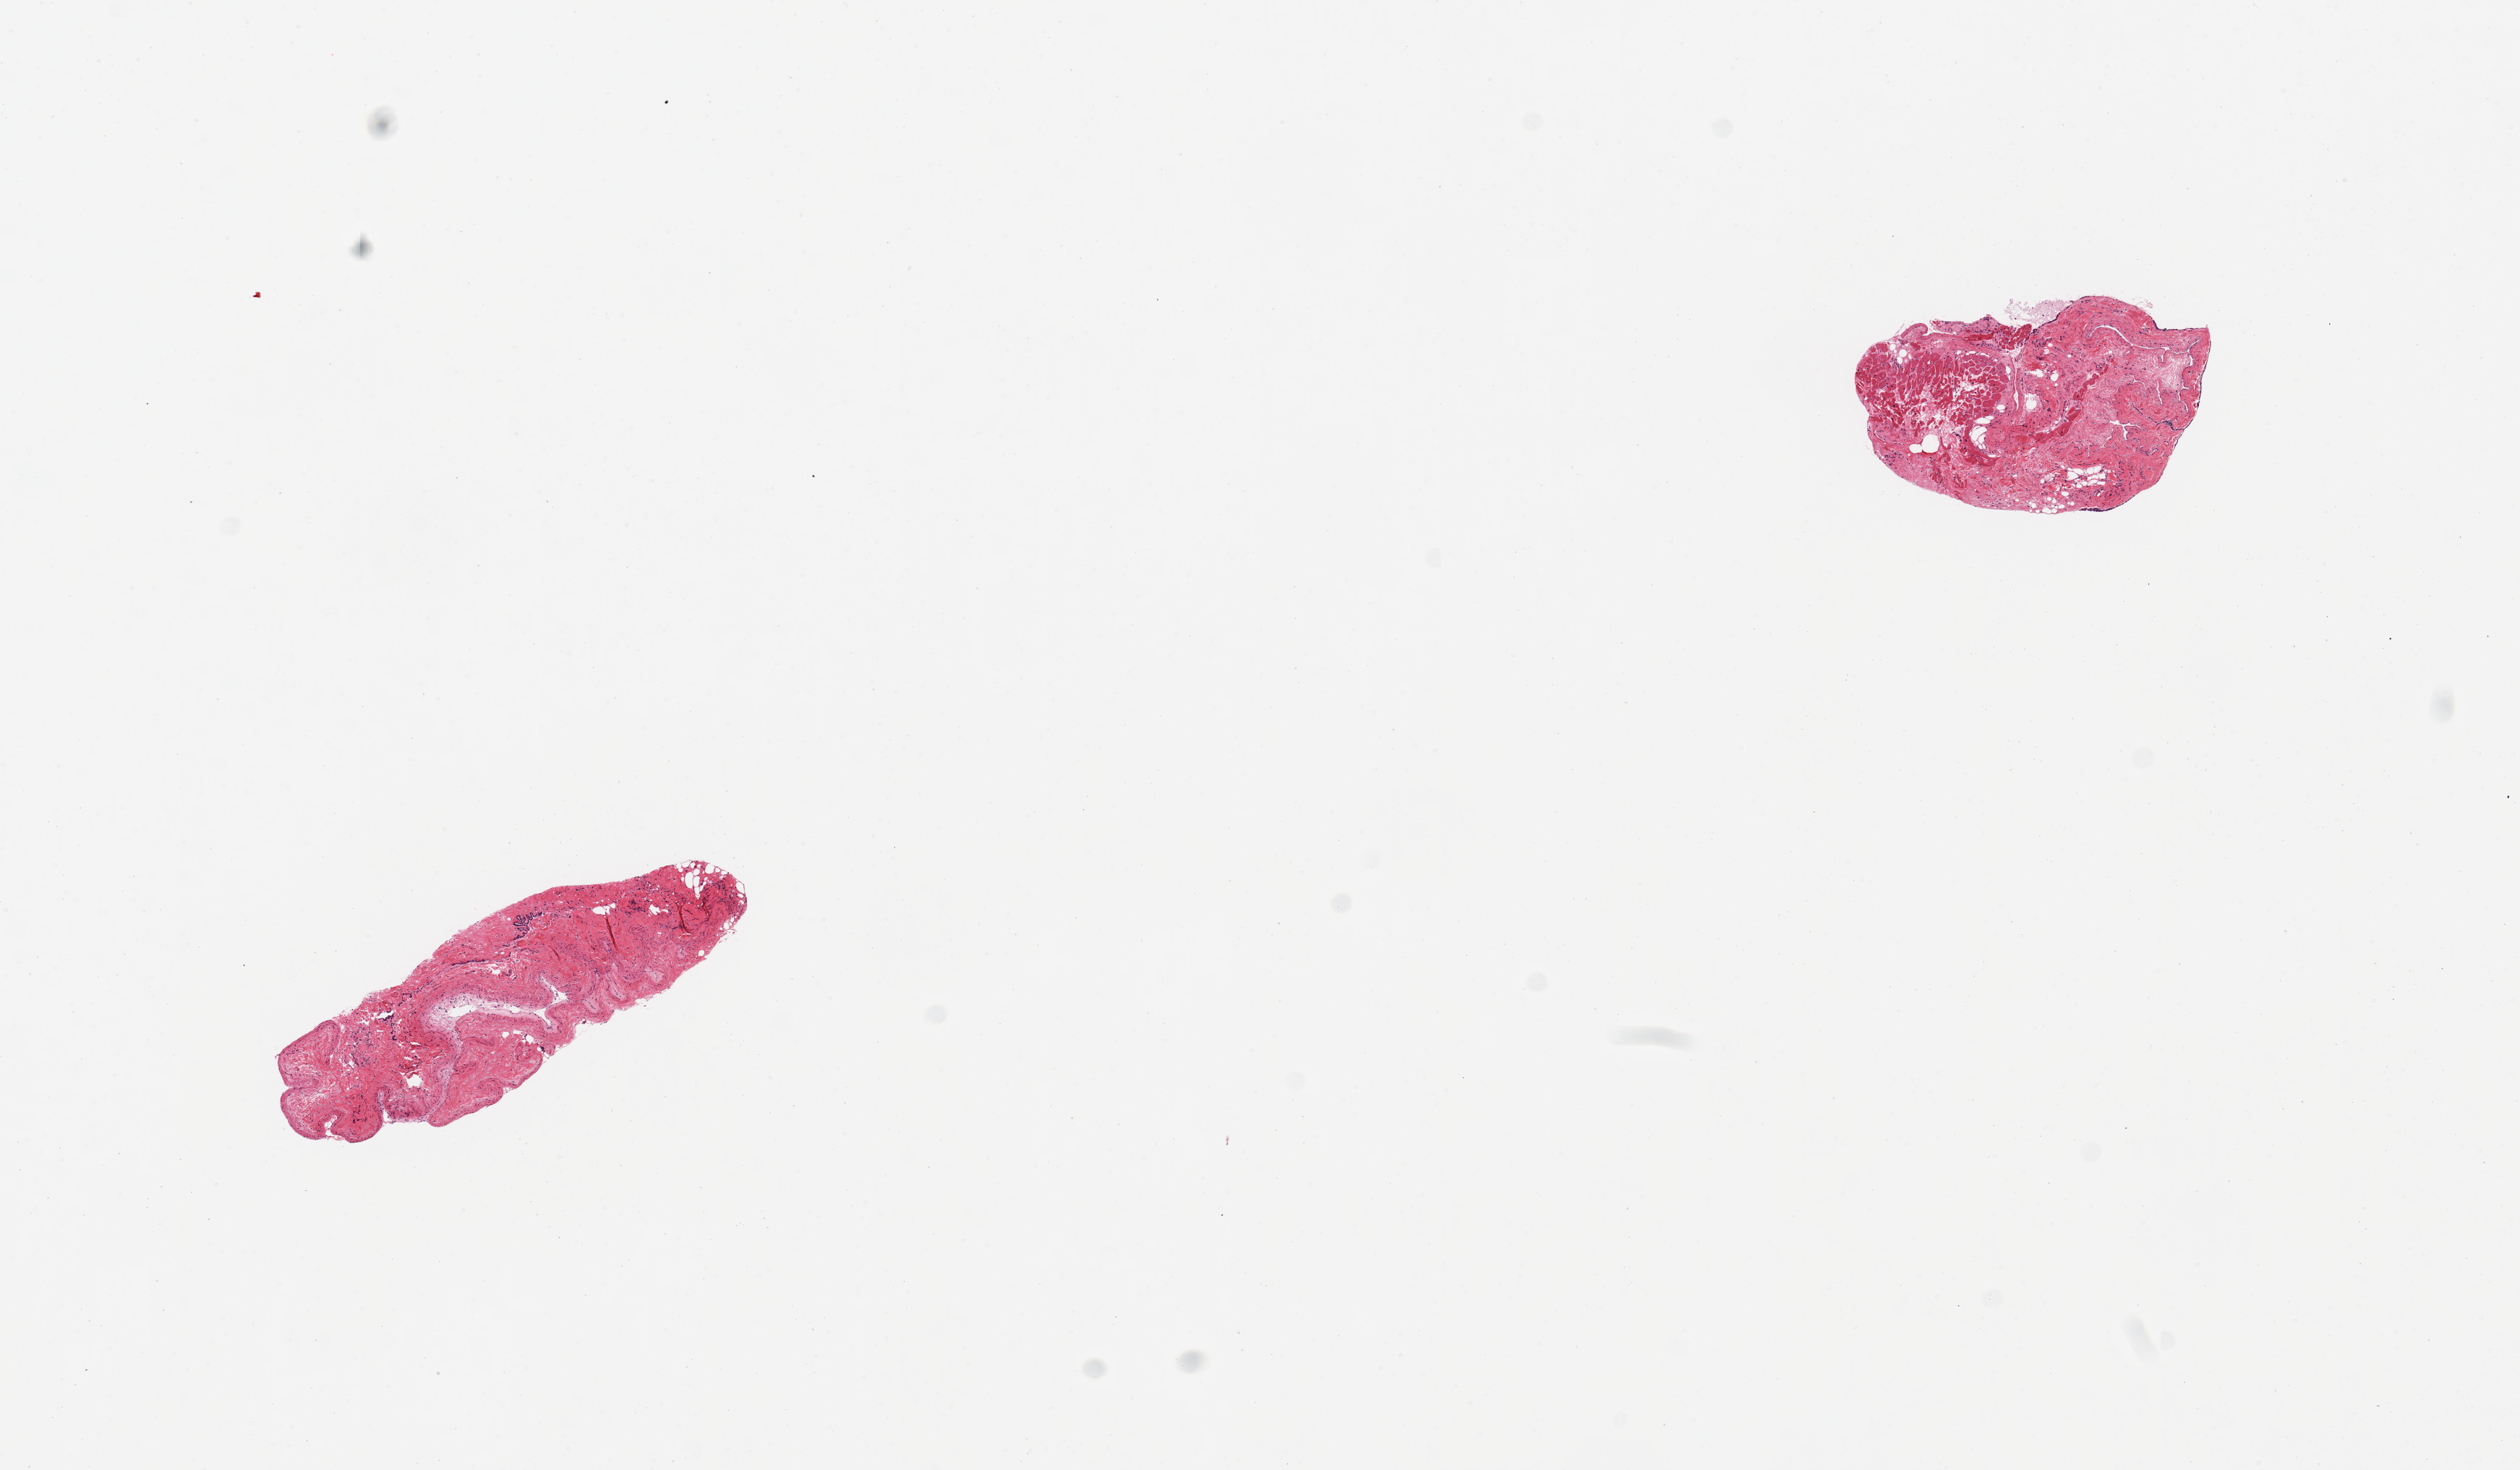
Digitized haematoxylin and eosin-stained section, shown as a low-resolution overview of the whole scanned area (about 13.8 x 8.0 mm); PAXgene-fixed paraffin-embedded (PFPE) section; section of coronary artery (target tissue); donor tissue sample. Male donor.
Reviewer comment on this tissue sample: 2 pieces, trace ? sinus, no artery, cardiac muscle/connective tissue.